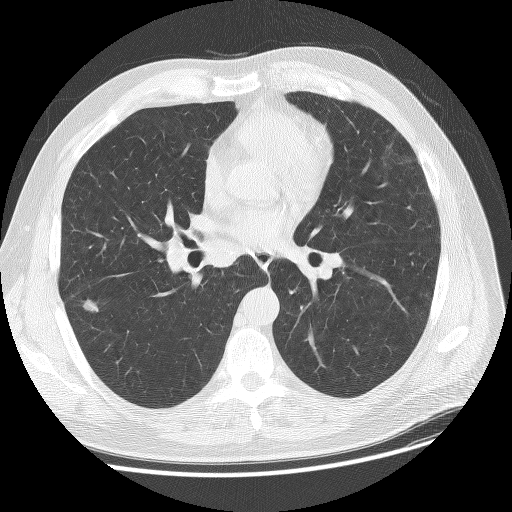
Low-dose screening chest CT, one axial slice. Lung window (W 1500 / L -600 HU). 512 × 512 image matrix, field of view 380 × 380 mm.
Annotated regions visible in this slice (expert manual segmentation):
- lesion 2 (tumor, lower lobe of right lung): box from (x=84, y=300) to (x=98, y=311) px